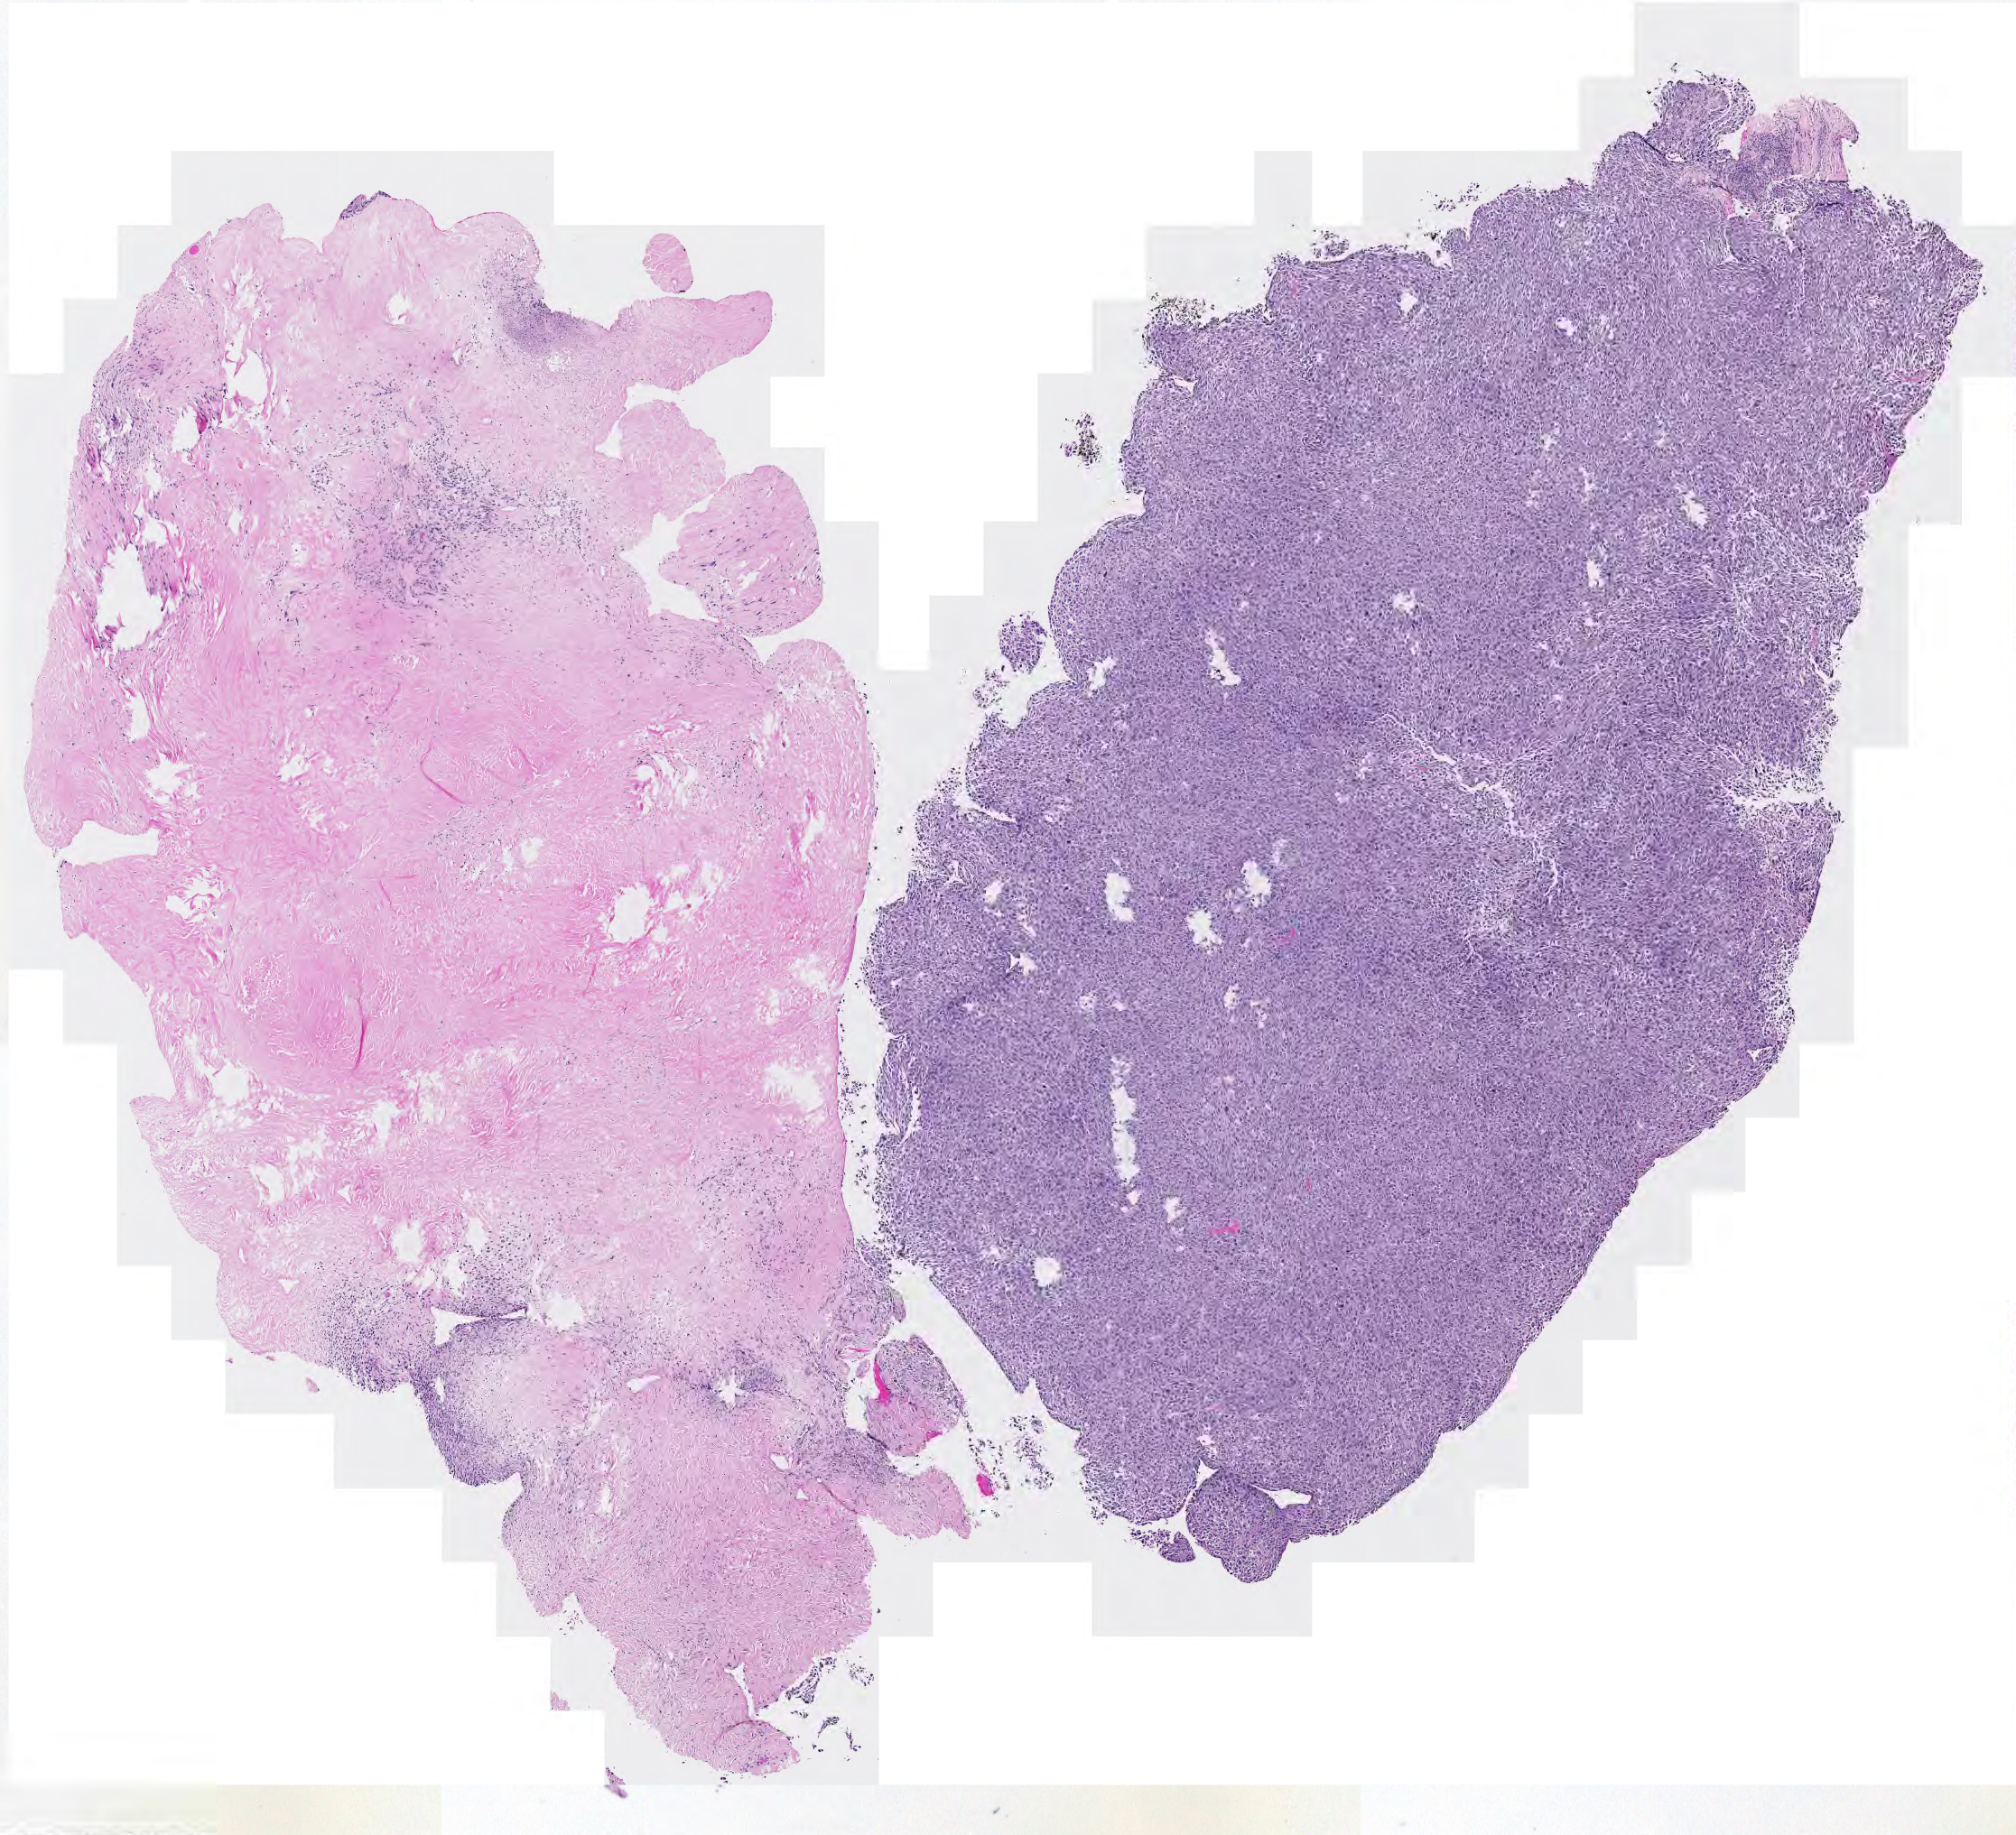
Digitized H&E-stained tissue section (whole slide), low-resolution overview of the scanned area, about 11.5 x 10.5 mm, tumour tissue sample. 81-year-old male patient.
Patient diagnosis (cohort enrolment): sarcoma (site not recorded at cohort level).